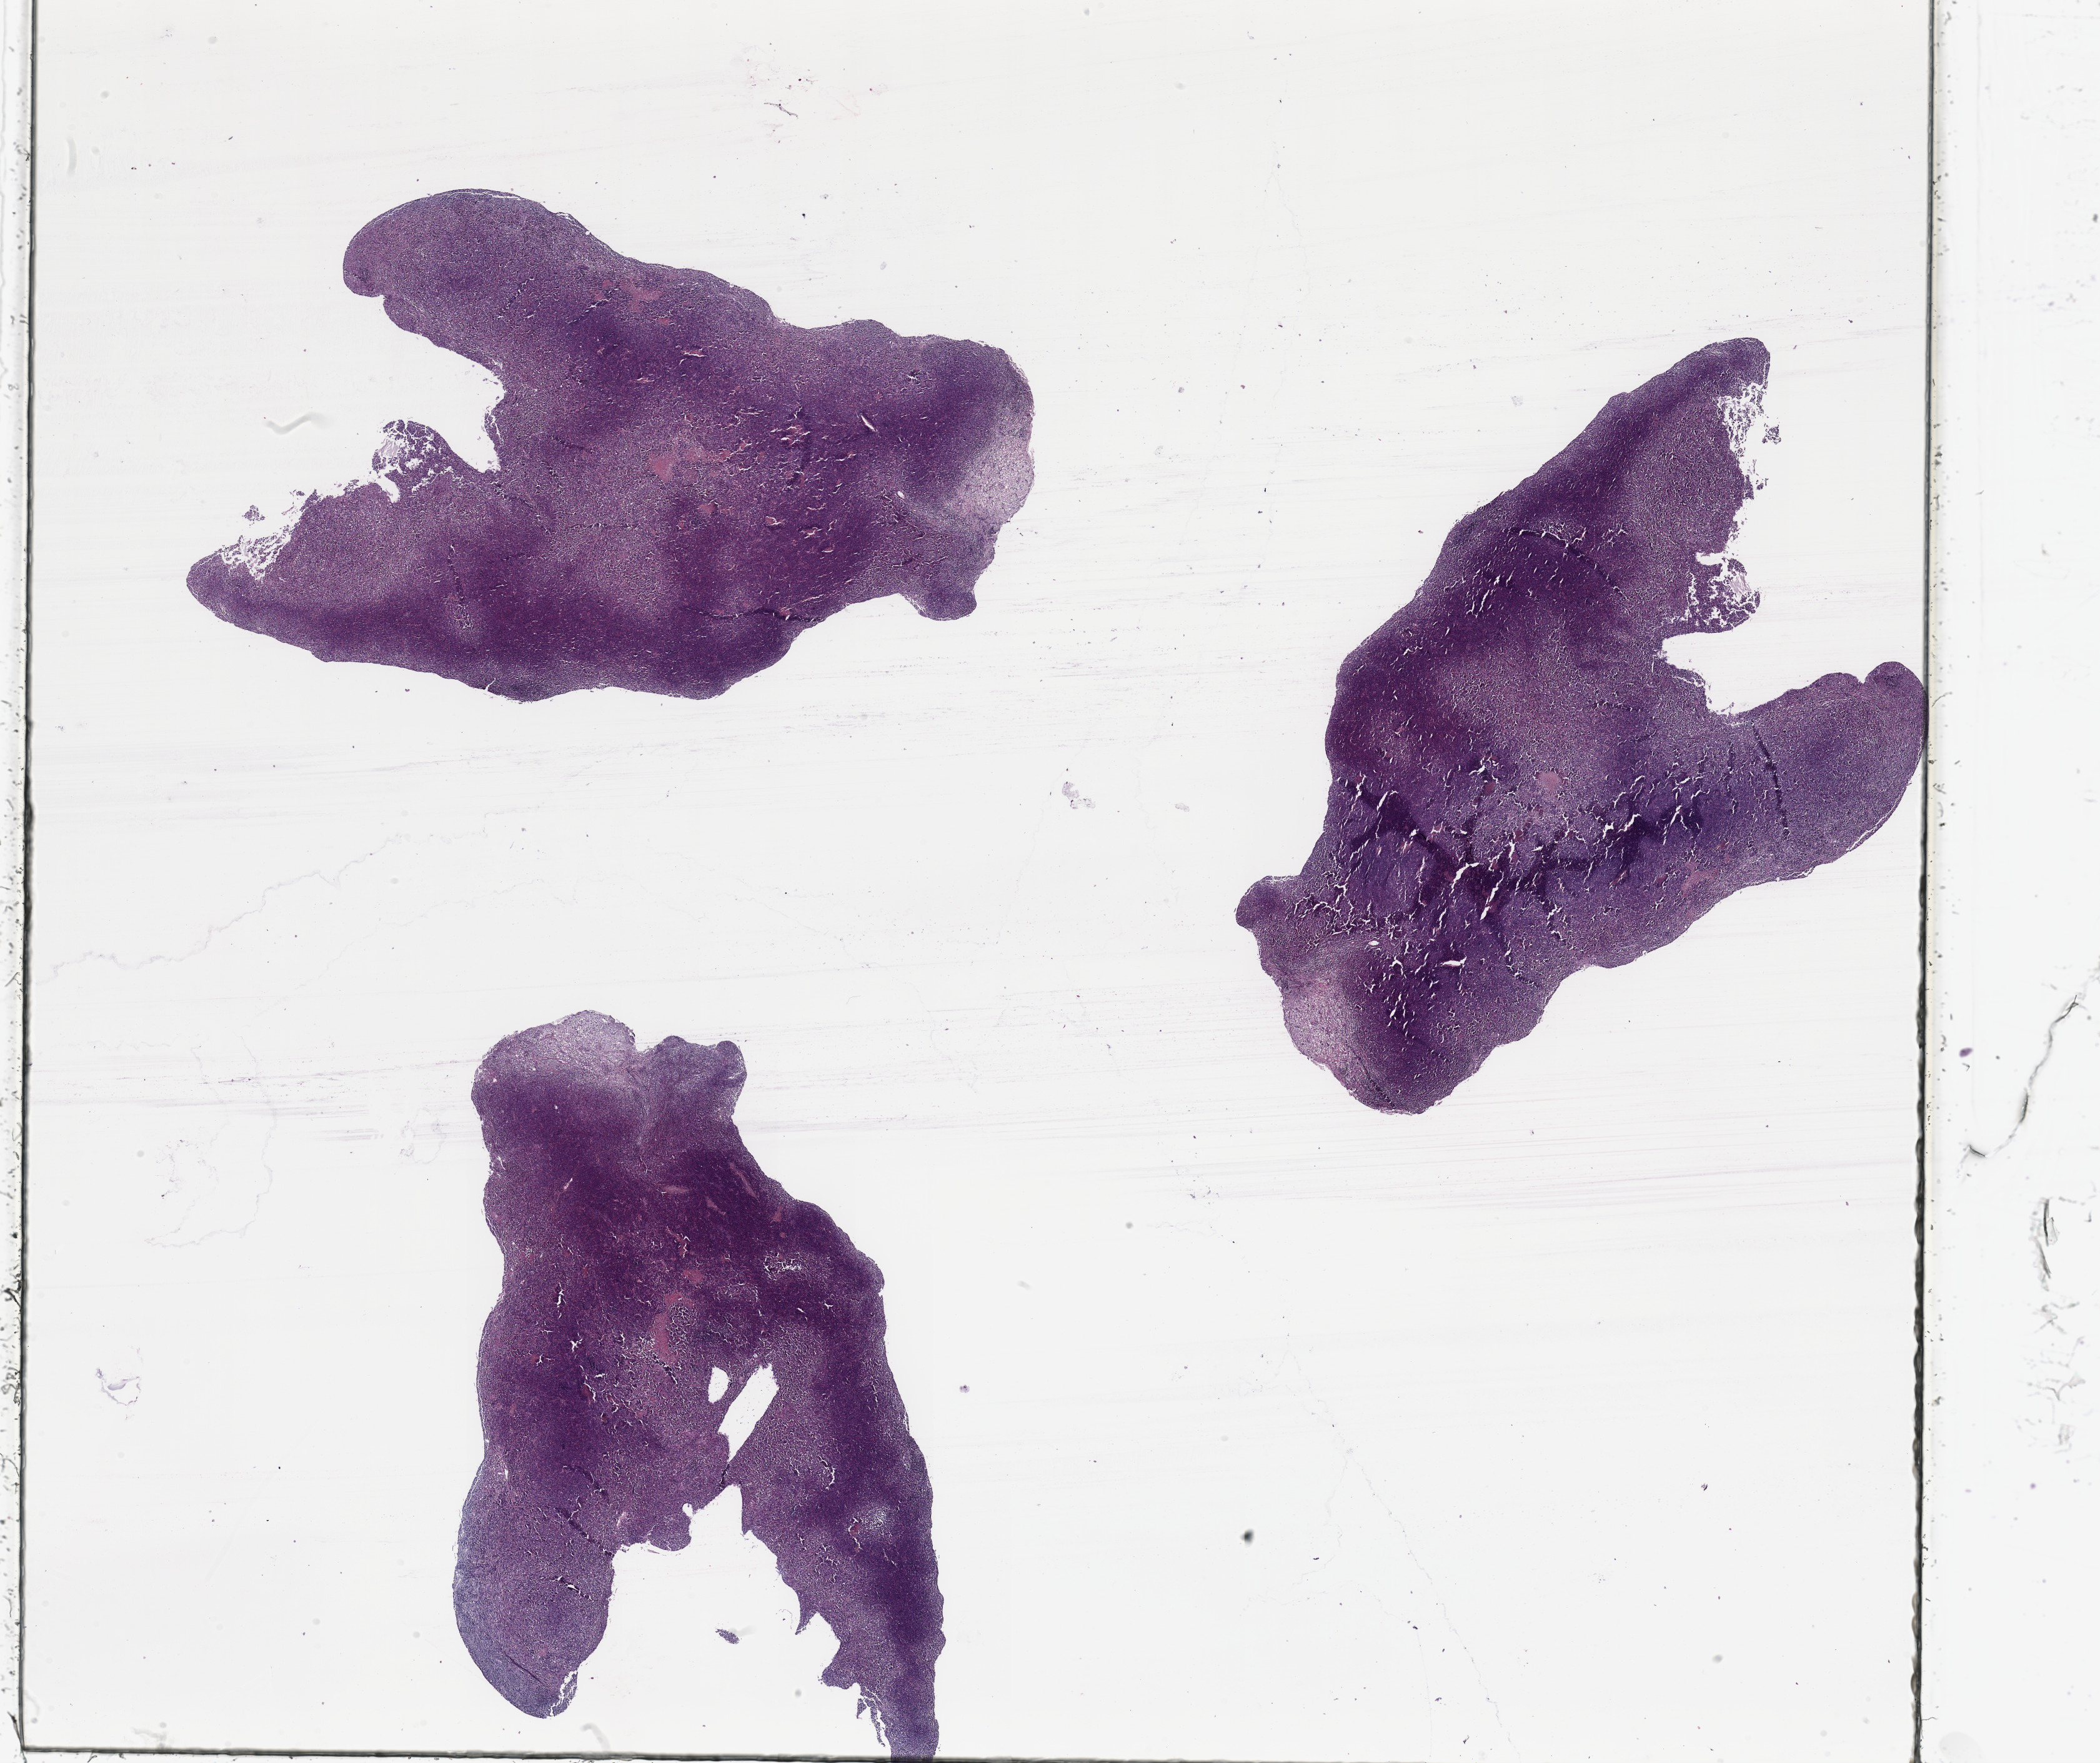
H&E whole-slide image — low-resolution overview of the scanned area, about 26.6 x 22.3 mm. Tumour tissue sample, sampled site: lymph node. Patient: female, age 46 years. Slide review estimates, as recorded: tumour nuclei 90%, necrosis 2%.
This section: metastatic tumour tissue. Primary tumour site (as recorded): extremities. Patient diagnosis: Malignant melanoma, NOS.